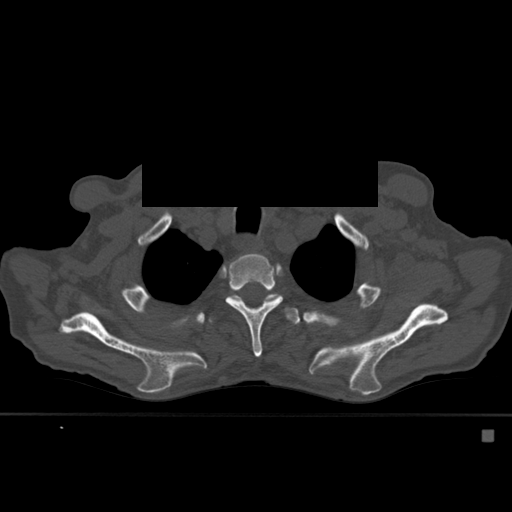
CT including the spine, one axial slice. Slice 430 of 527 in the series (ordered by position). Bone window (W 1800 / L 400 HU). 1.5 mm slice thickness. 512 × 512 image matrix, field of view 373 × 373 mm. Male patient, age 78 years. From the clinical record (not read from this slice): primary cancer: prostate.
Structures marked on this image (semi-automatic segmentation, software-assisted and operator-edited):
- T3 vertebra: bounding box [x1, y1, x2, y2] px = [225, 254, 283, 358]
- T4 vertebra: [208, 293, 300, 325]